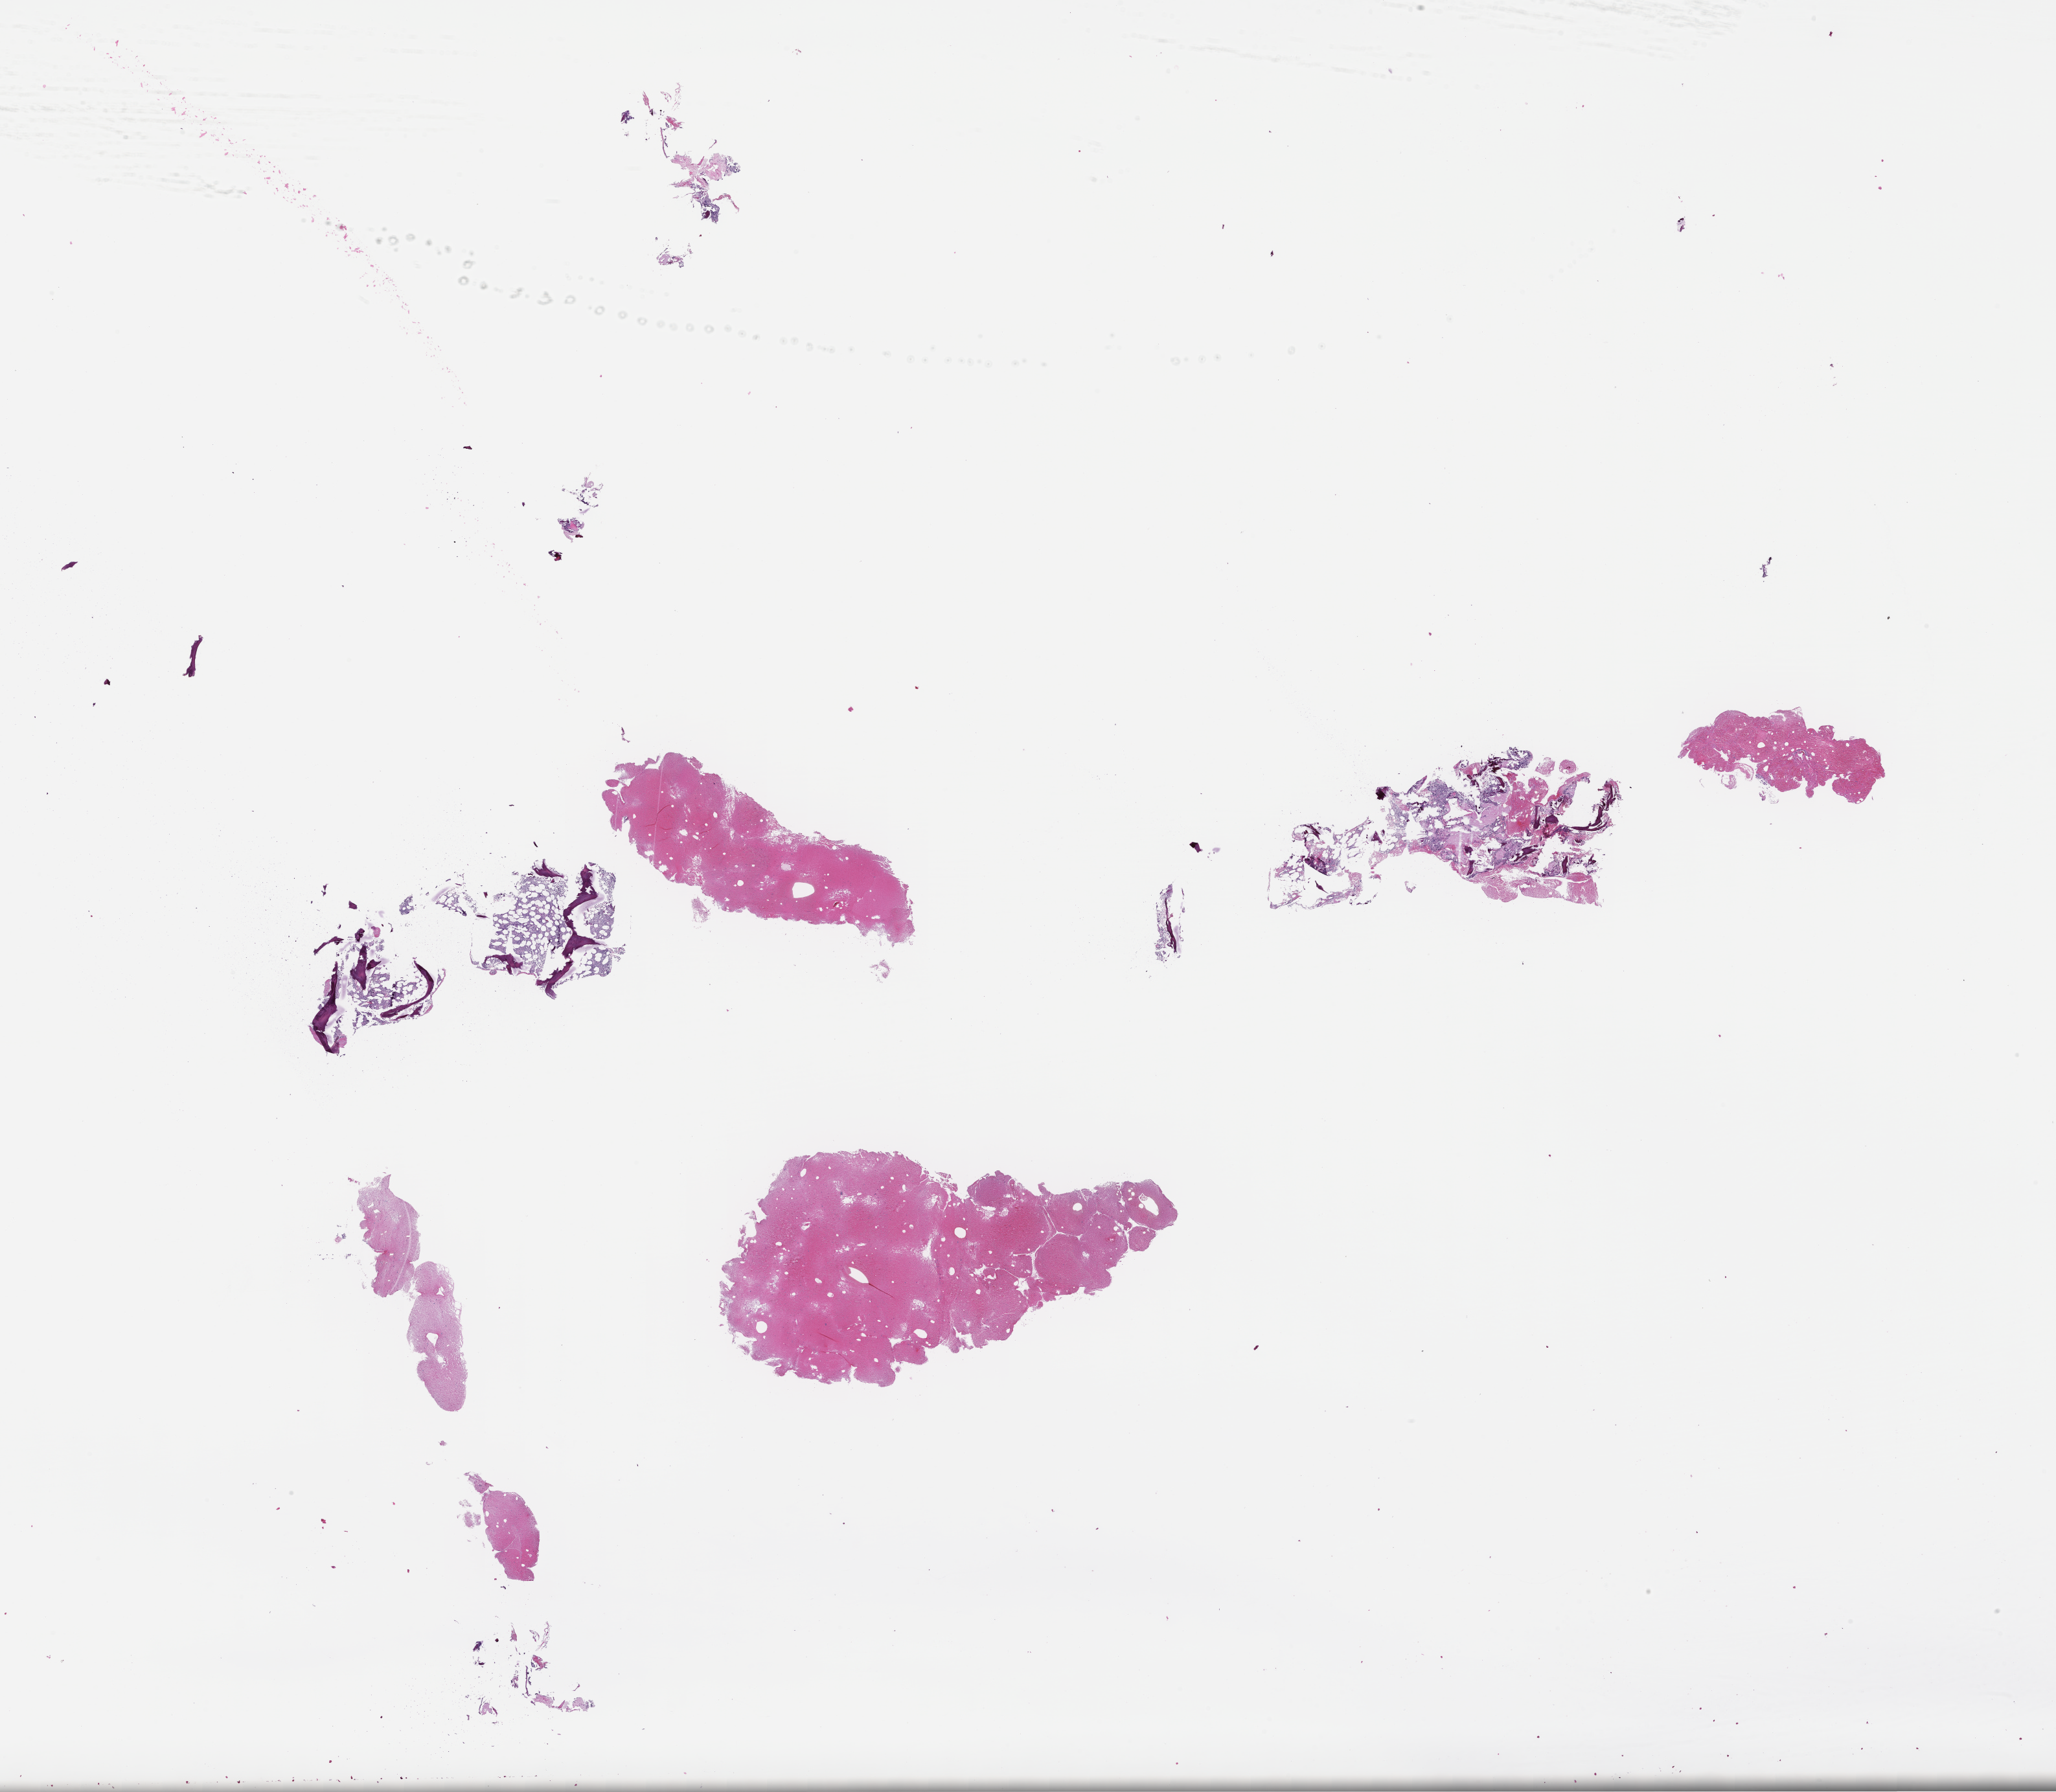
H&E whole-slide image, whole scanned area (about 25.6 x 22.3 mm) shown as a low-resolution overview. Formalin-fixed paraffin-embedded section. Collected at disease progression. Patient sex: male.
- this section: metastatic tumor tissue
- primary diagnosis of the patient: Plasma Cell Myeloma